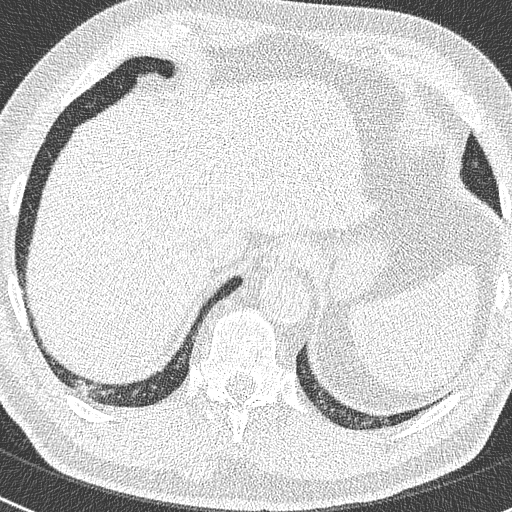
Low-dose screening chest CT, axial slice; second screening round (one year after baseline); lung window (W 1500 / L -600 HU); 2 mm slice thickness; lung (sharp) reconstruction kernel (B50f); slice 234 of 299 in the series; 512 × 512 image matrix, field of view 300 × 300 mm. Male participant, aged 63 years at enrolment. Former smoker at enrolment.
Expert-annotated lung lesion, bounding box [x1, y1, x2, y2] px = [67, 378, 101, 404]. Screening reader's record for this exam: no non-calcified nodule ≥4 mm recorded. Official screen result: negative screen, no significant abnormalities.